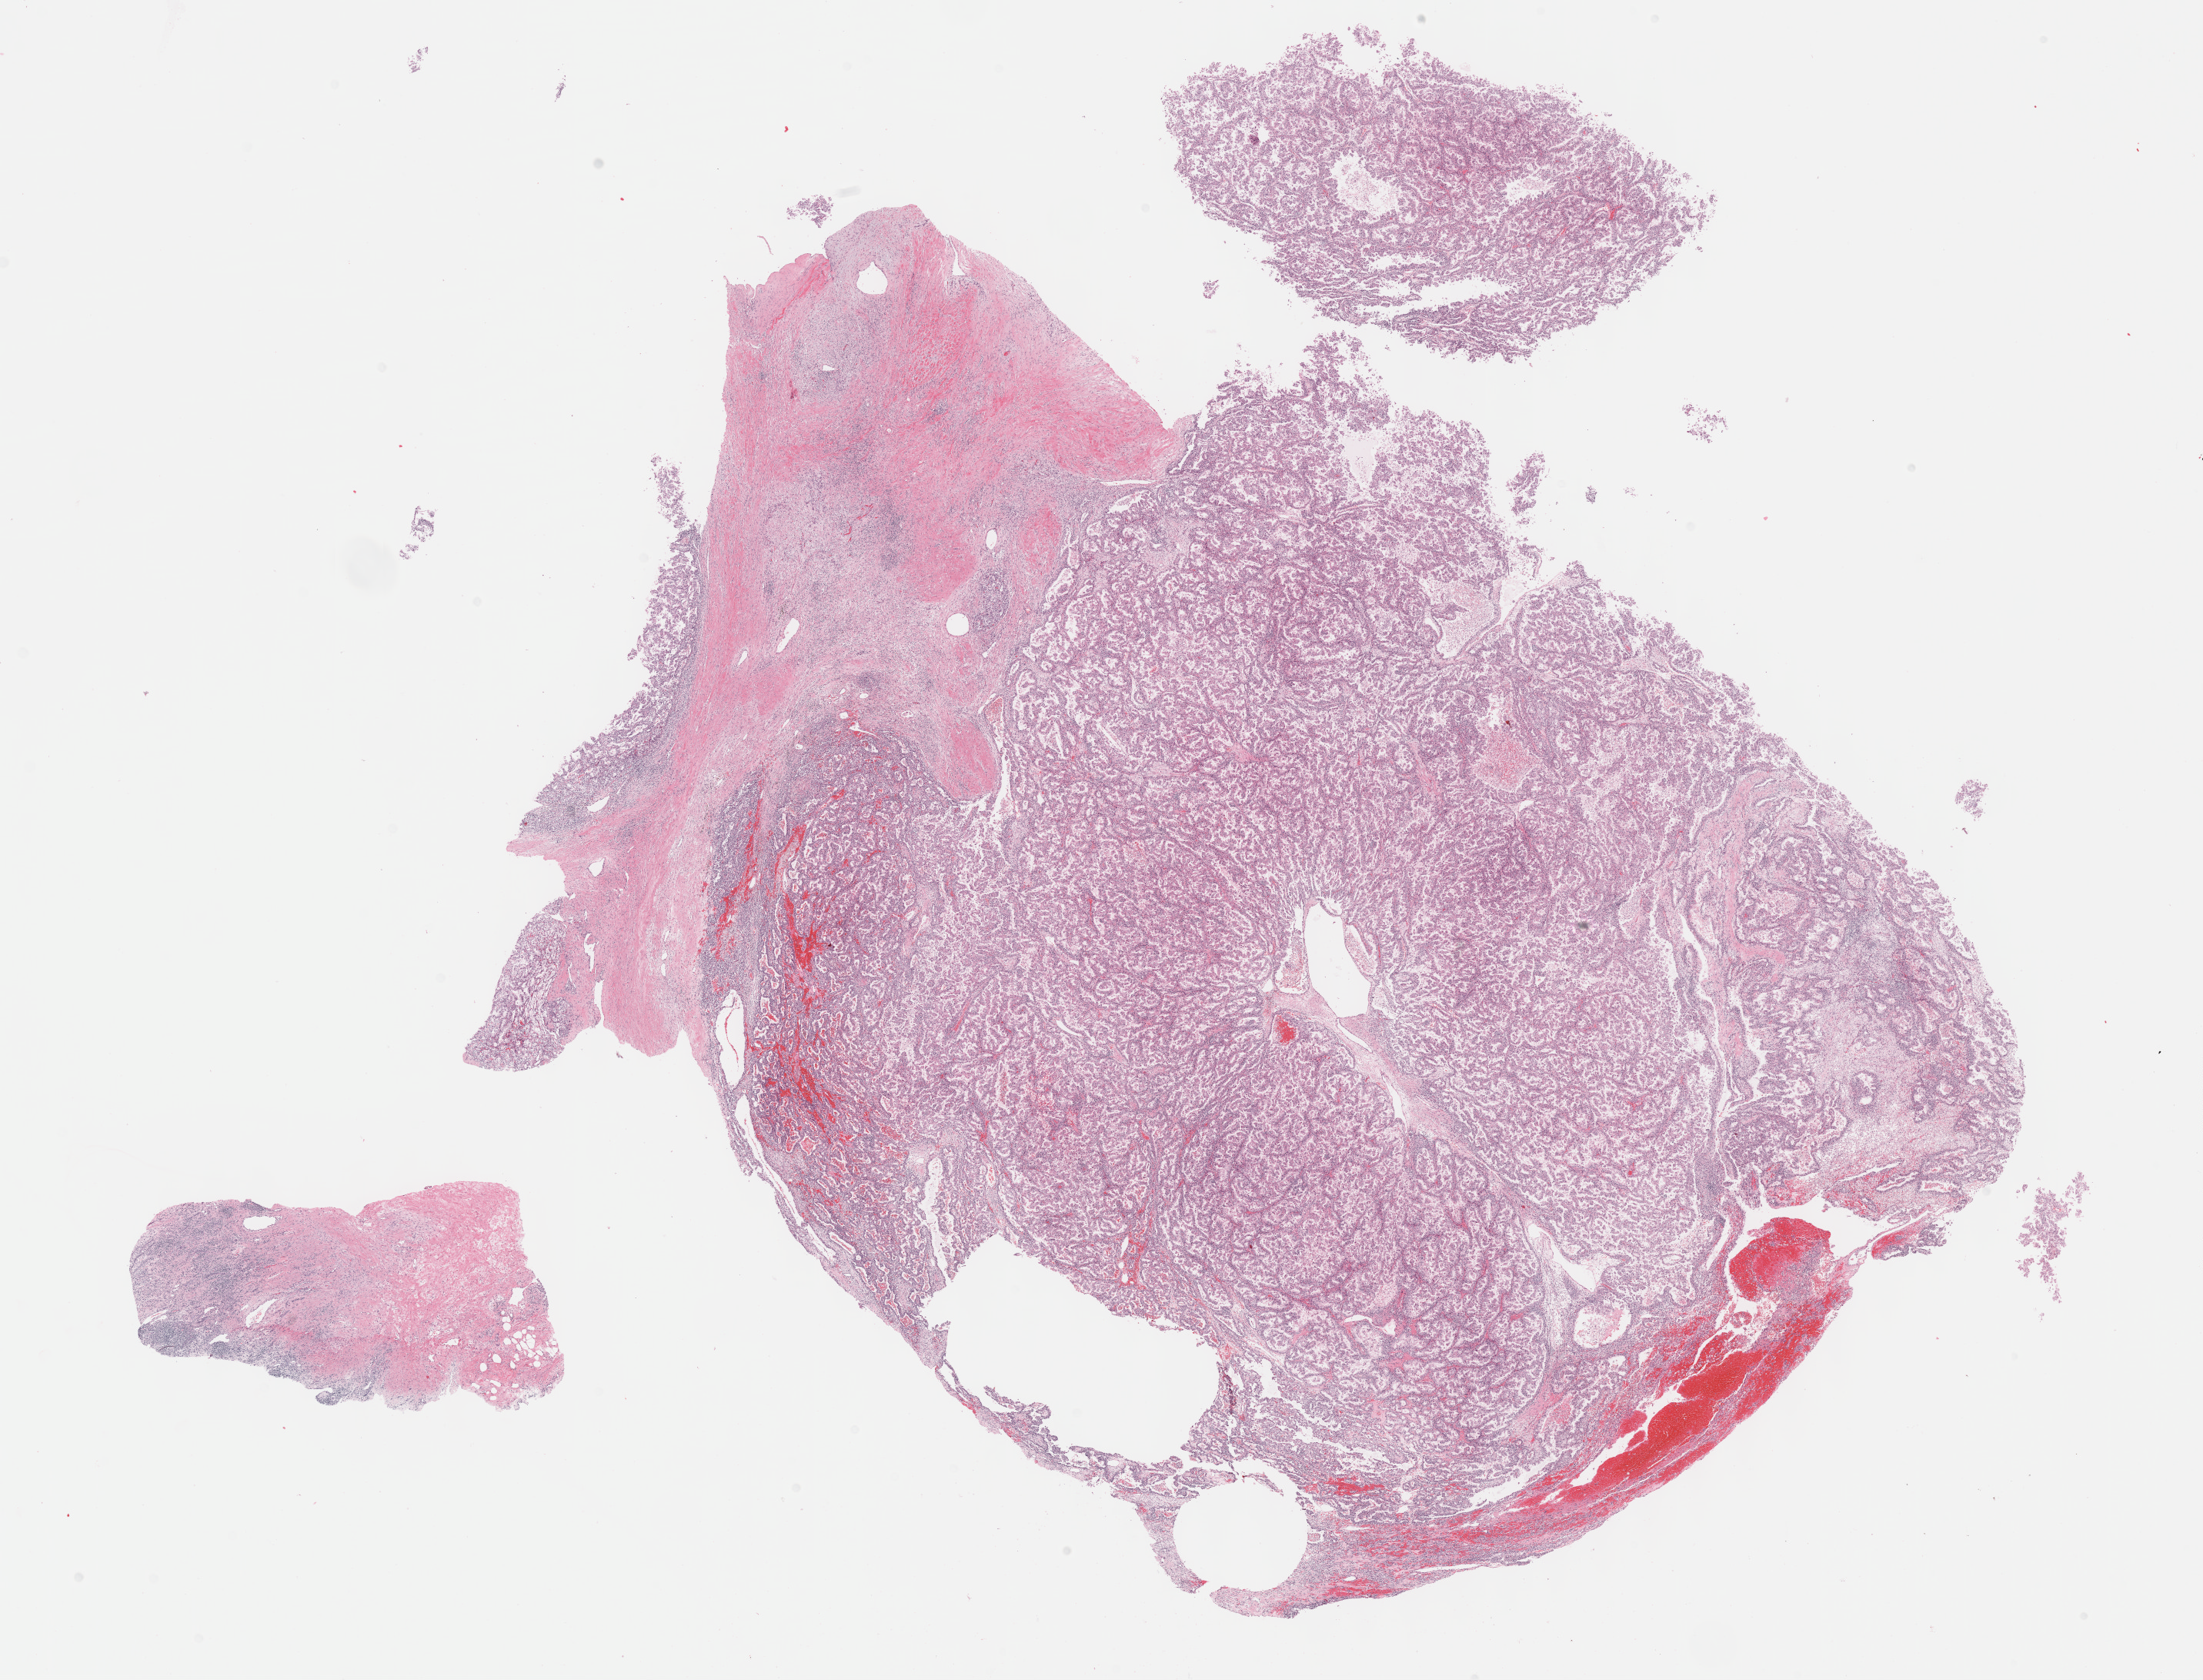
Whole-slide histology image, Hematoxylin and eosin (H&E) stained — whole scanned area (about 23.2 x 17.7 mm) shown as a low-resolution overview. Formalin-fixed paraffin-embedded (FFPE) diagnostic section. Sample: primary tumour, kidney. Male, age 55 years at initial diagnosis.
• diagnosis: Papillary adenocarcinoma, NOS
• laterality: left
• lymph nodes positive (case pathology): 0 of 33 examined
• AJCC pathologic stage: II (6th edition)